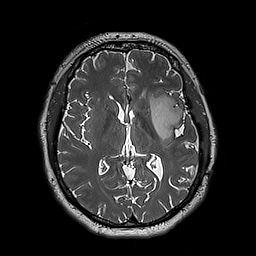
Brain MRI from a brain-tumour surgery series, one axial slice; slice 101 of 192 in the series (ordered by position); 1 mm slice thickness; 256 × 256 image matrix, field of view 250 × 250 mm. From the clinical record (not read from this slice): histopathology: Astrocytoma; WHO grade: 3; IDH mutation: yes; tumour location: Left Insular.
Annotated regions visible in this slice (outlined manually by an expert reader):
- tumour: bounding box <148,96,184,141> (left, top, right, bottom; pixels)